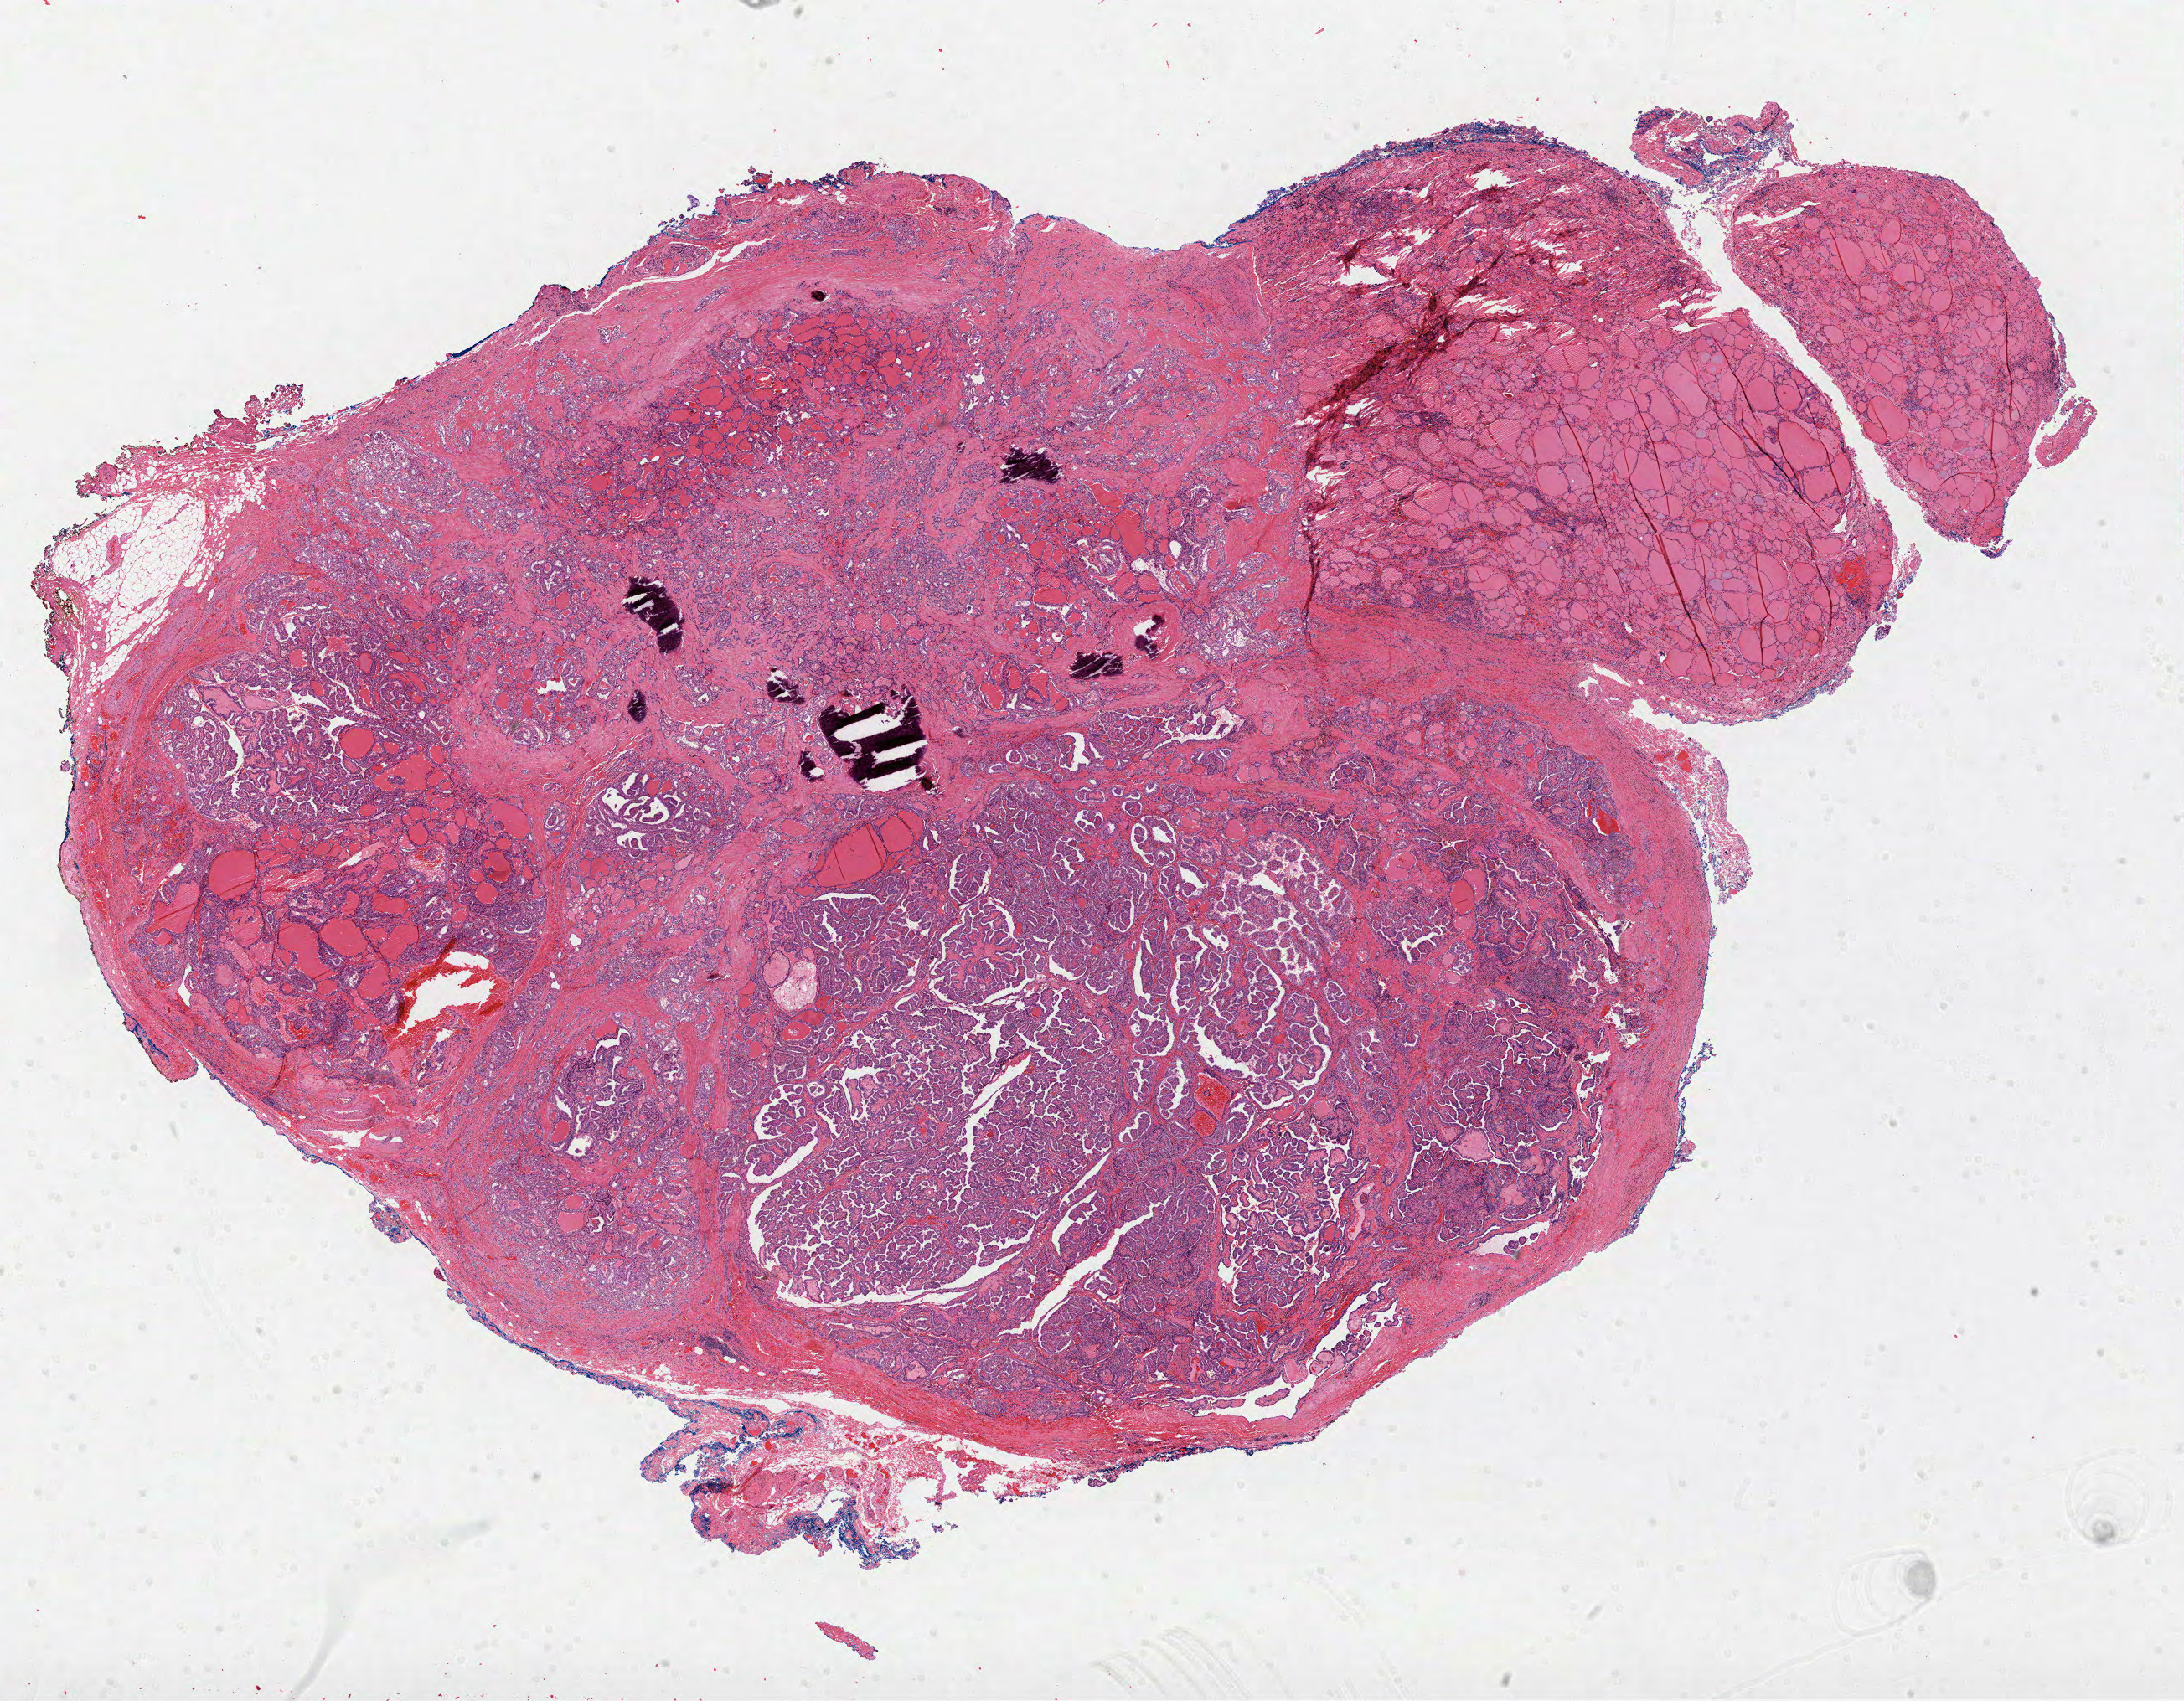
Digitized H&E-stained tissue section (whole slide), a low-resolution overview of the entire scanned area, about 21.0 x 16.4 mm (from a 40x scan), formalin-fixed paraffin-embedded (FFPE) diagnostic section, thyroid, primary tumour sample. Female patient; age at initial diagnosis 50 years.
Histologic diagnosis: Papillary adenocarcinoma, NOS (thyroid gland). Lymph nodes positive (case pathology): 2 of 2 examined. AJCC pathologic stage: III (7th edition).